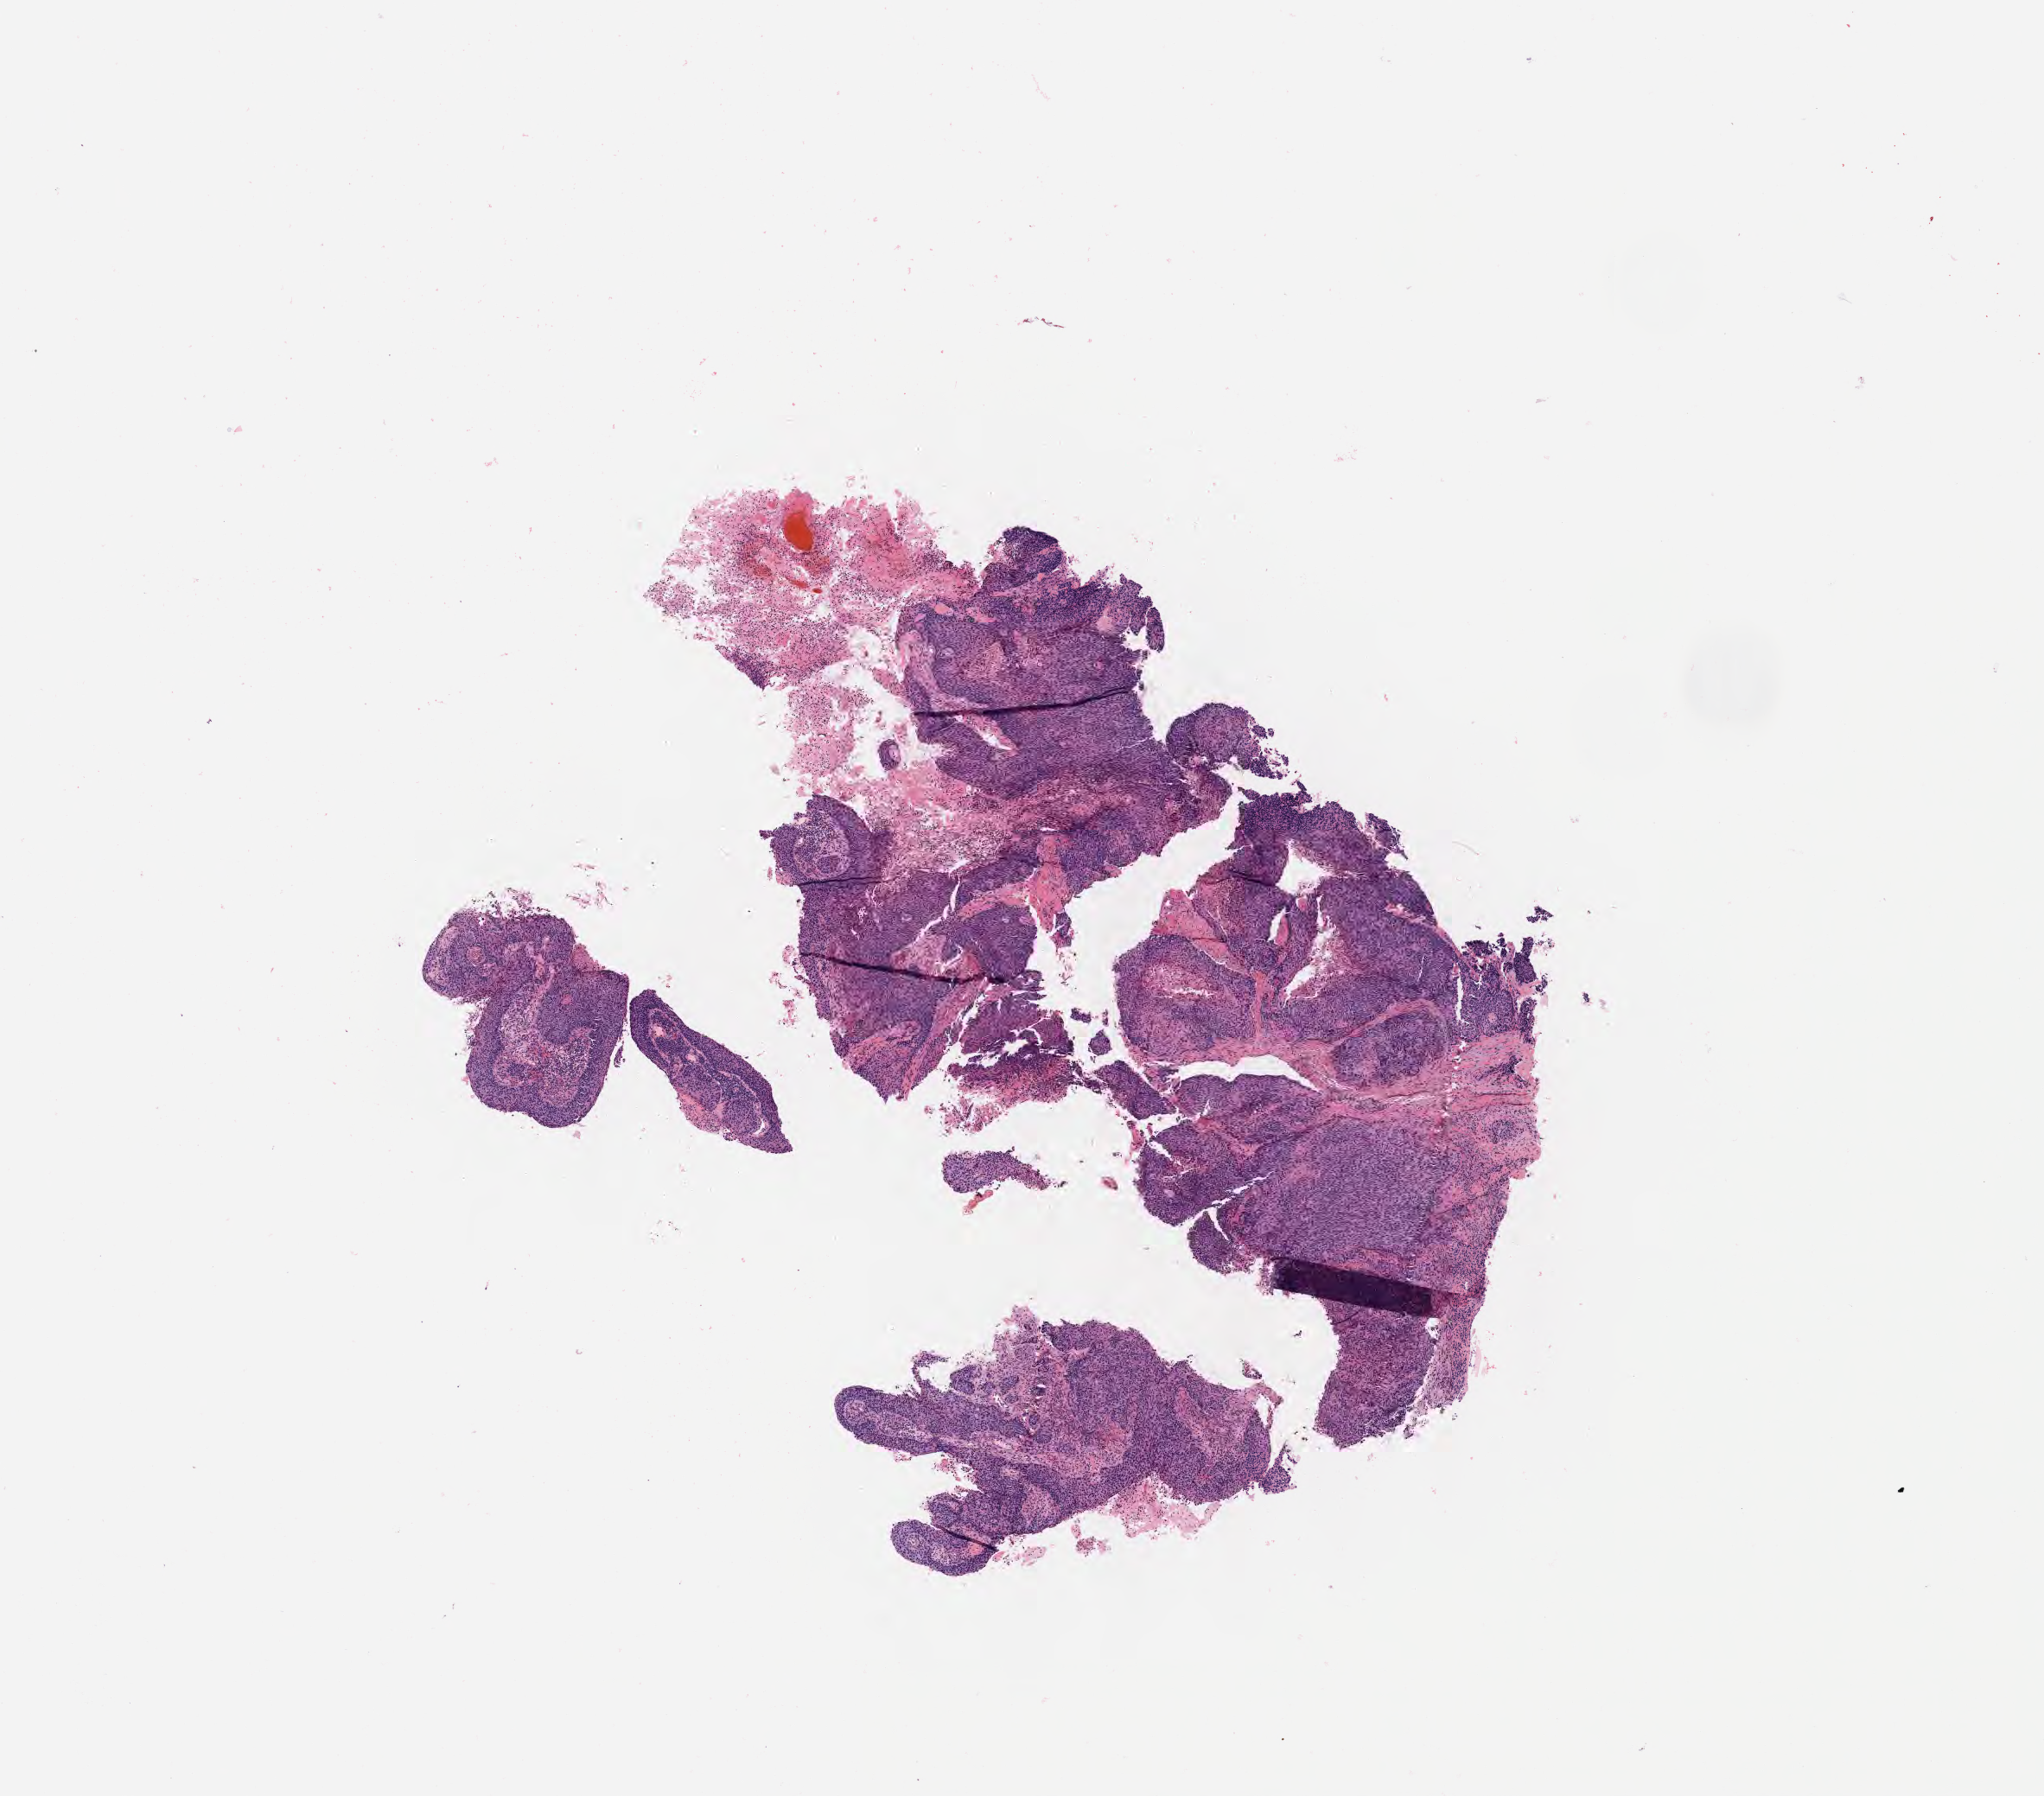
Whole-slide image, hematoxylin and eosin (H&E) stain — shown as a low-resolution overview of the whole scanned area (about 9.6 x 8.4 mm), tumor tissue, site: cervix. Patient female; 57 years old.
Diagnosis: Squamous cell carcinoma, large cell, nonkeratinizing, NOS.